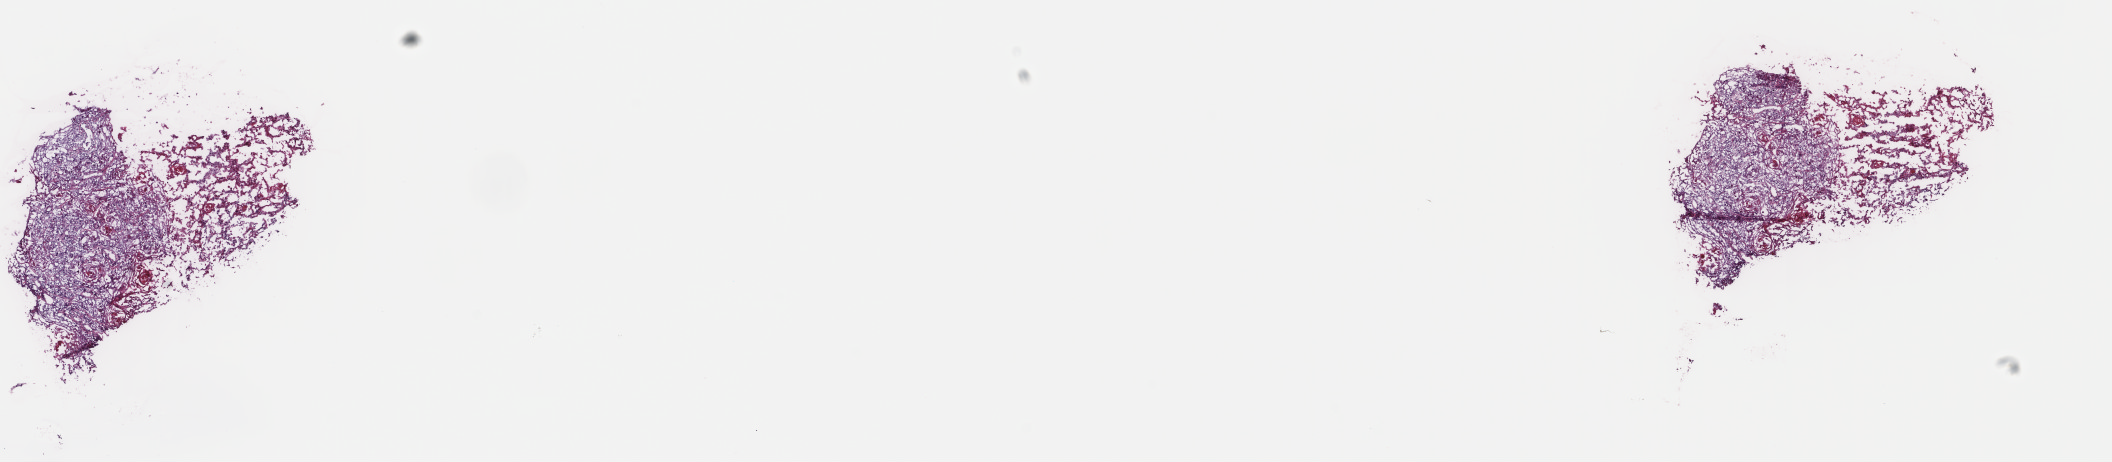
Digitized H&E-stained tissue section (whole slide) — a low-resolution overview of the entire scanned area, about 16.8 x 3.7 mm (slide scanned at 40x); frozen section; bladder, primary tumour sample. Patient: female, age at initial diagnosis 56 years.
Pathologic diagnosis: Transitional cell carcinoma.